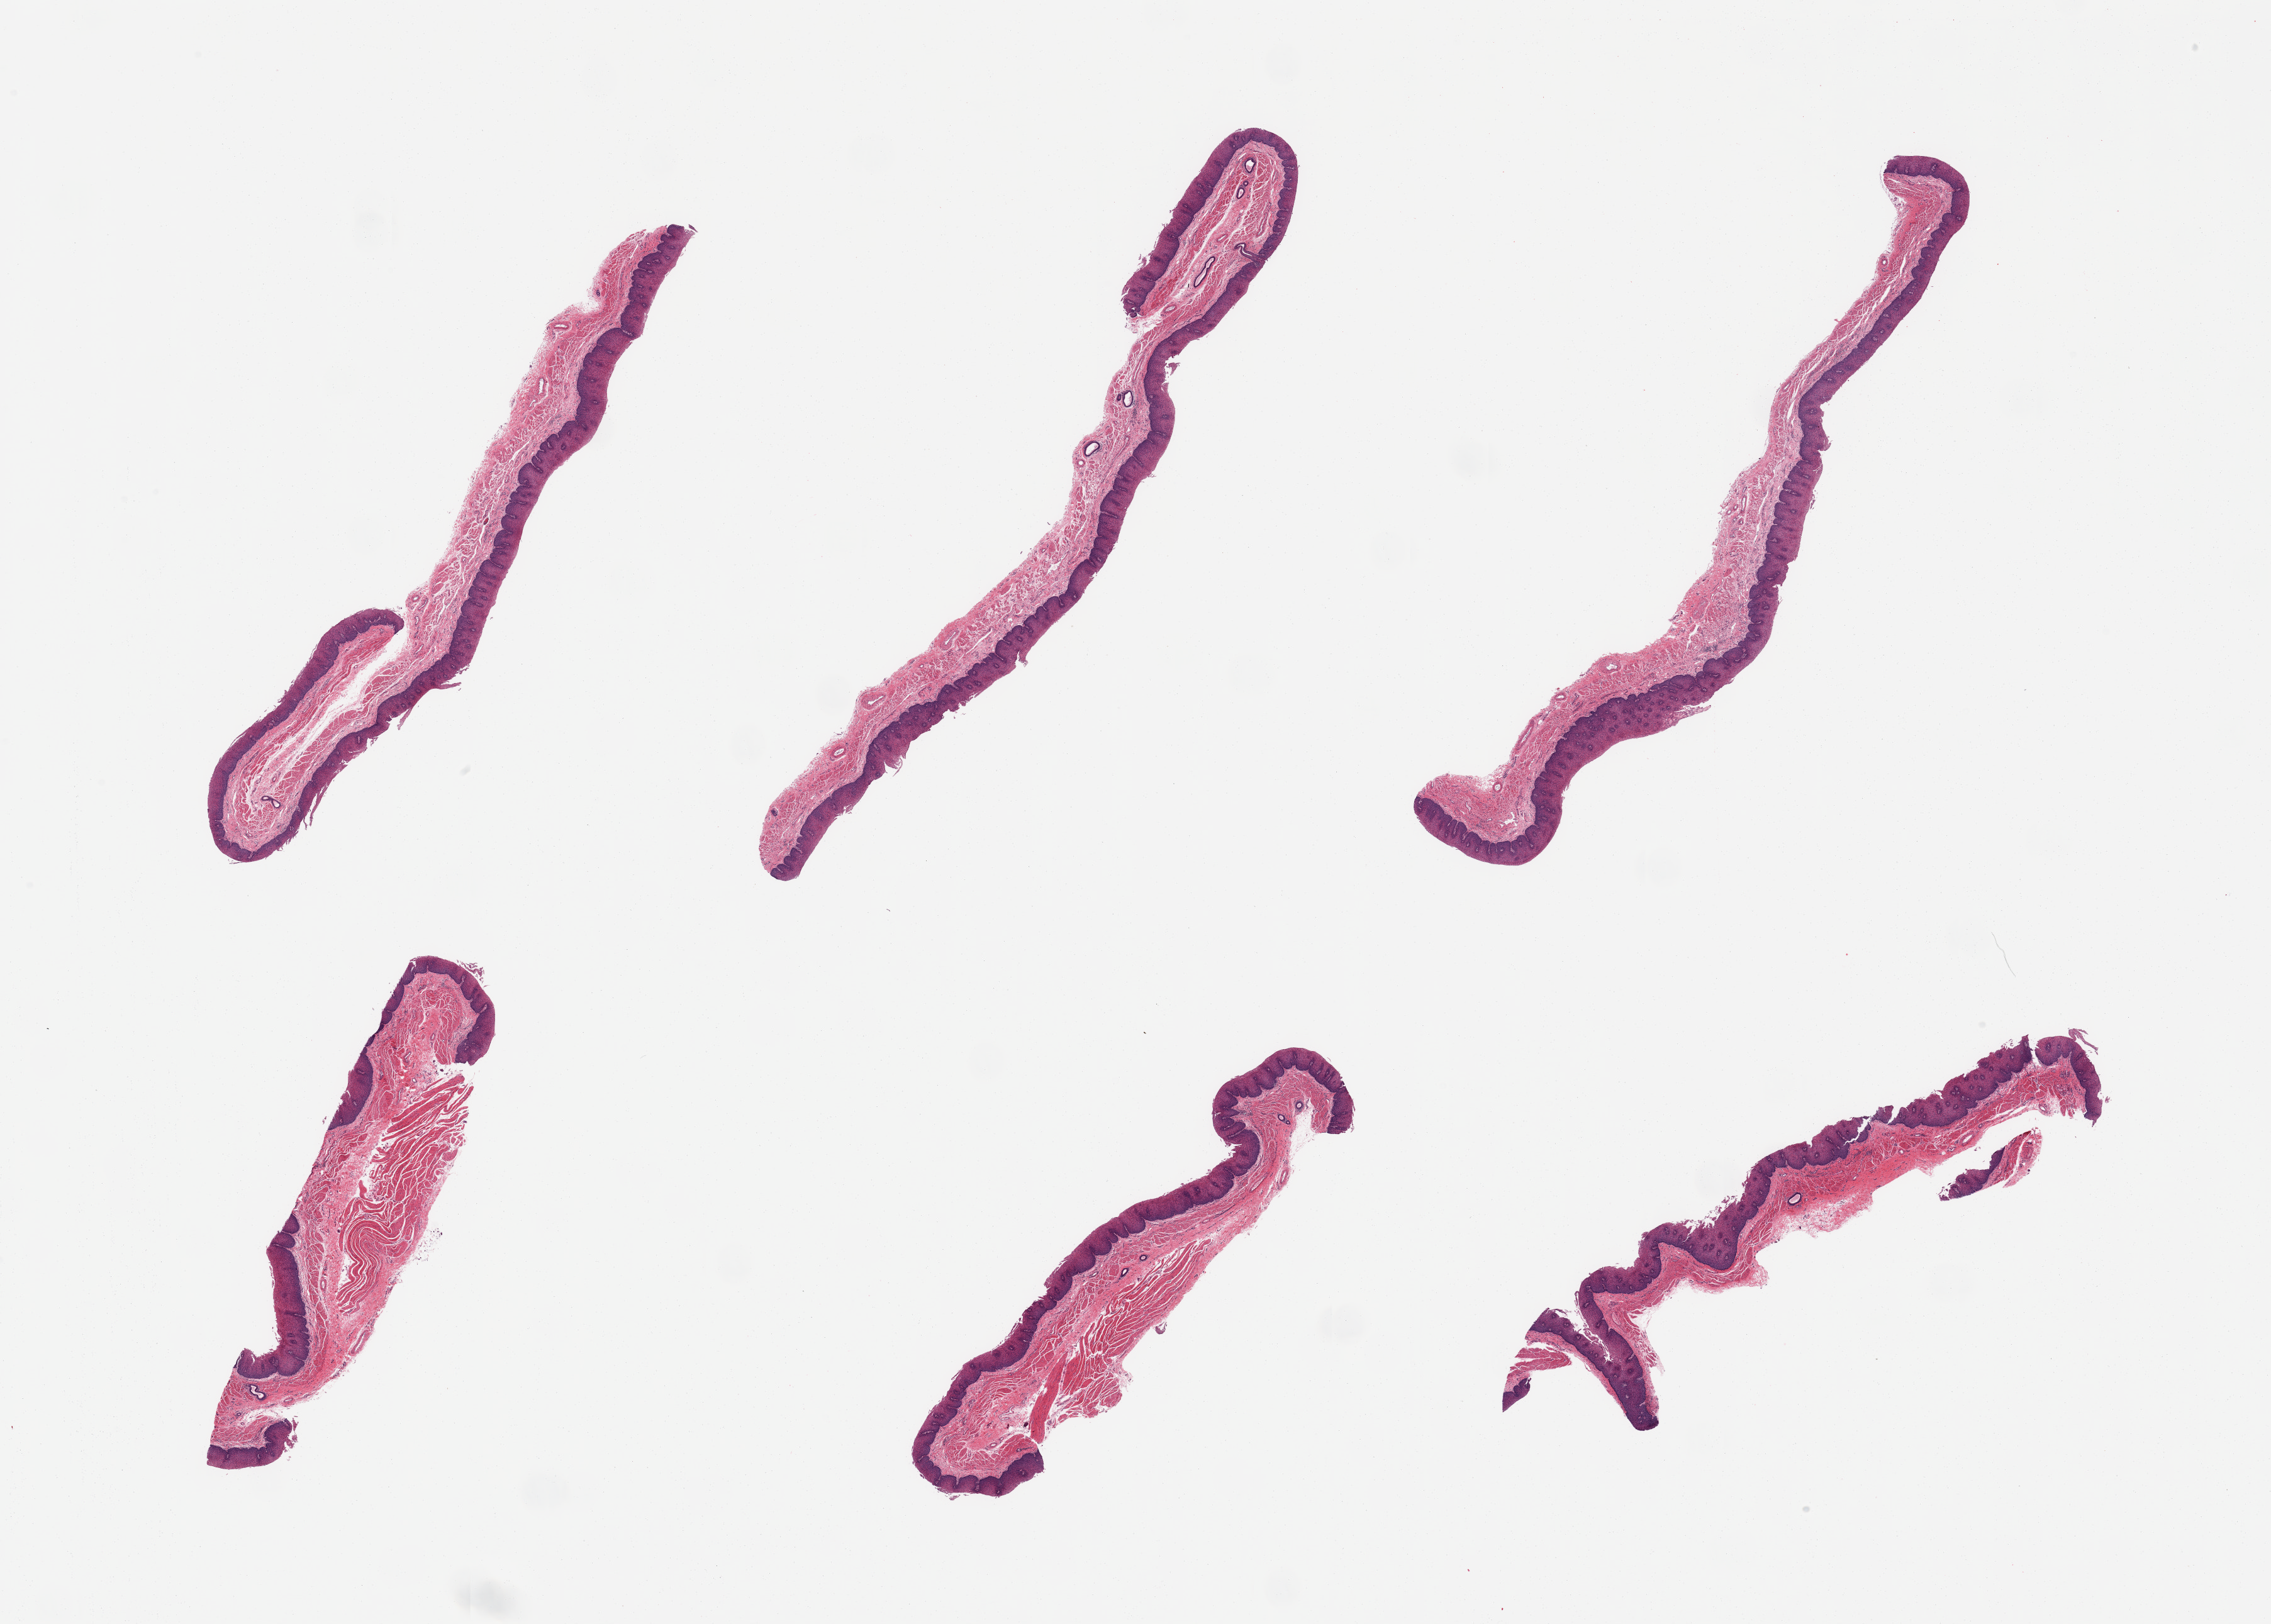
Whole-slide image, hematoxylin and eosin (H&E) stain — whole scanned area (about 28.5 x 20.4 mm, from a 20x scan) shown as a low-resolution overview; PAXgene-fixed paraffin-embedded (PFPE) section; sampled site (target tissue): esophageal mucous membrane; donor tissue sample. Female donor.
- reviewer comment on this tissue sample: 6 pieces; ~0.25mm squamous epithelium; 2 pieces have some muscularis propria; crystals like those in stomach also in submucosa of esophagus